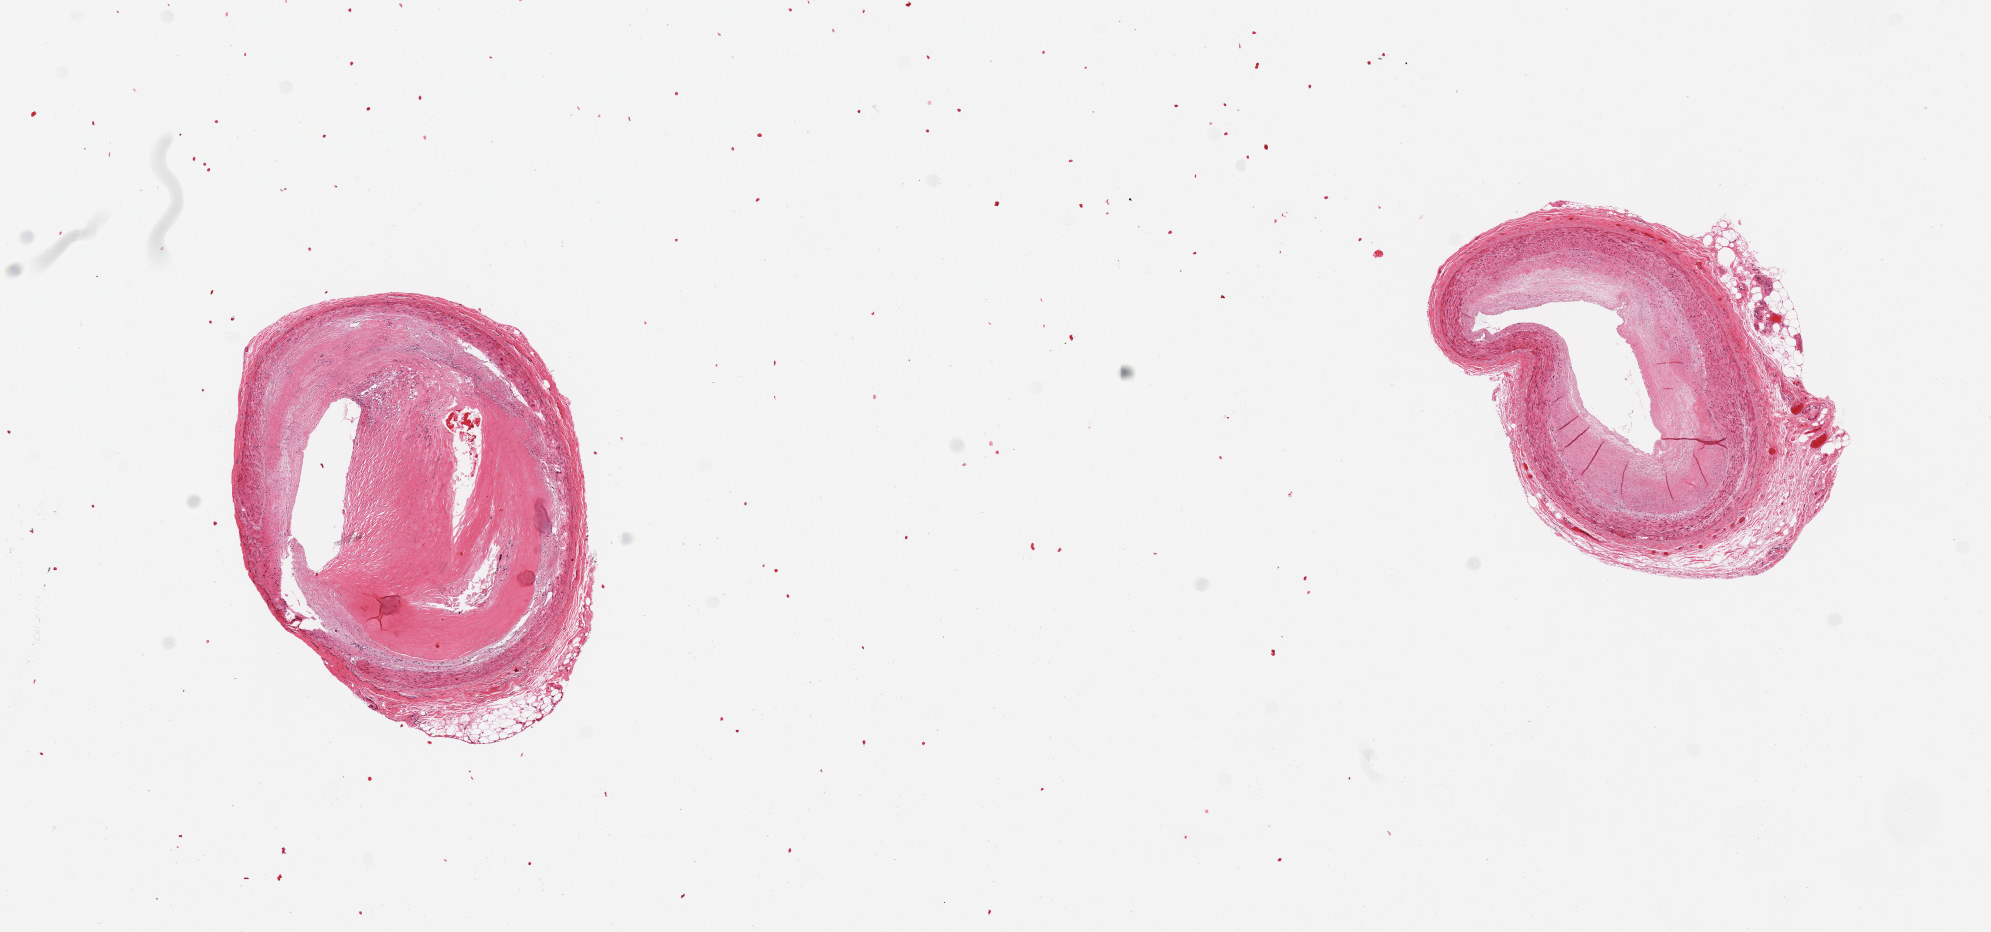
Digitized H&E-stained section, shown as a low-resolution overview of the whole scanned area (about 15.8 x 7.4 mm, from a 20x scan). PAXgene-fixed paraffin-embedded (PFPE) section. Target tissue: coronary artery. Donor tissue sample. Donor sex: male.
Pathologist's review note for this sample: 2 pieces, subtotally occlusive atherosis, focal ~0.5mm adherent fat.